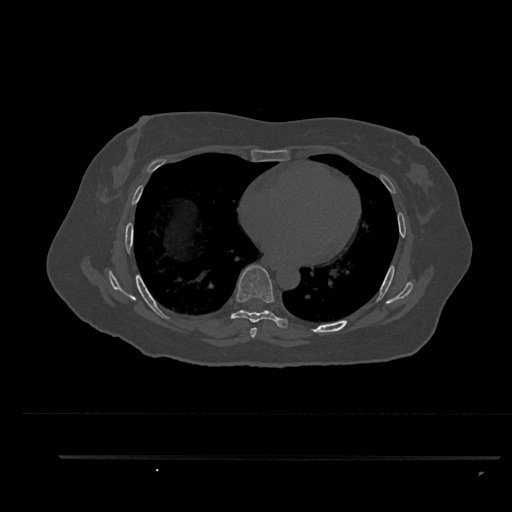
CT including the spine, one axial slice. Position 509 of 797 along the scan axis. 120 kVp. Bone window (W 1800 / L 400 HU). 0.5 mm slice thickness. 512 × 512 image matrix, field of view 408 × 408 mm. Female patient, age 44 years. From the clinical record (not read from this slice): primary cancer: renal.
Outlined on this slice (semi-automatically segmented with operator editing):
- T6 vertebra: box from (x=250, y=328) to (x=257, y=338) px
- T7 vertebra: (x=231, y=265)–(x=288, y=328)